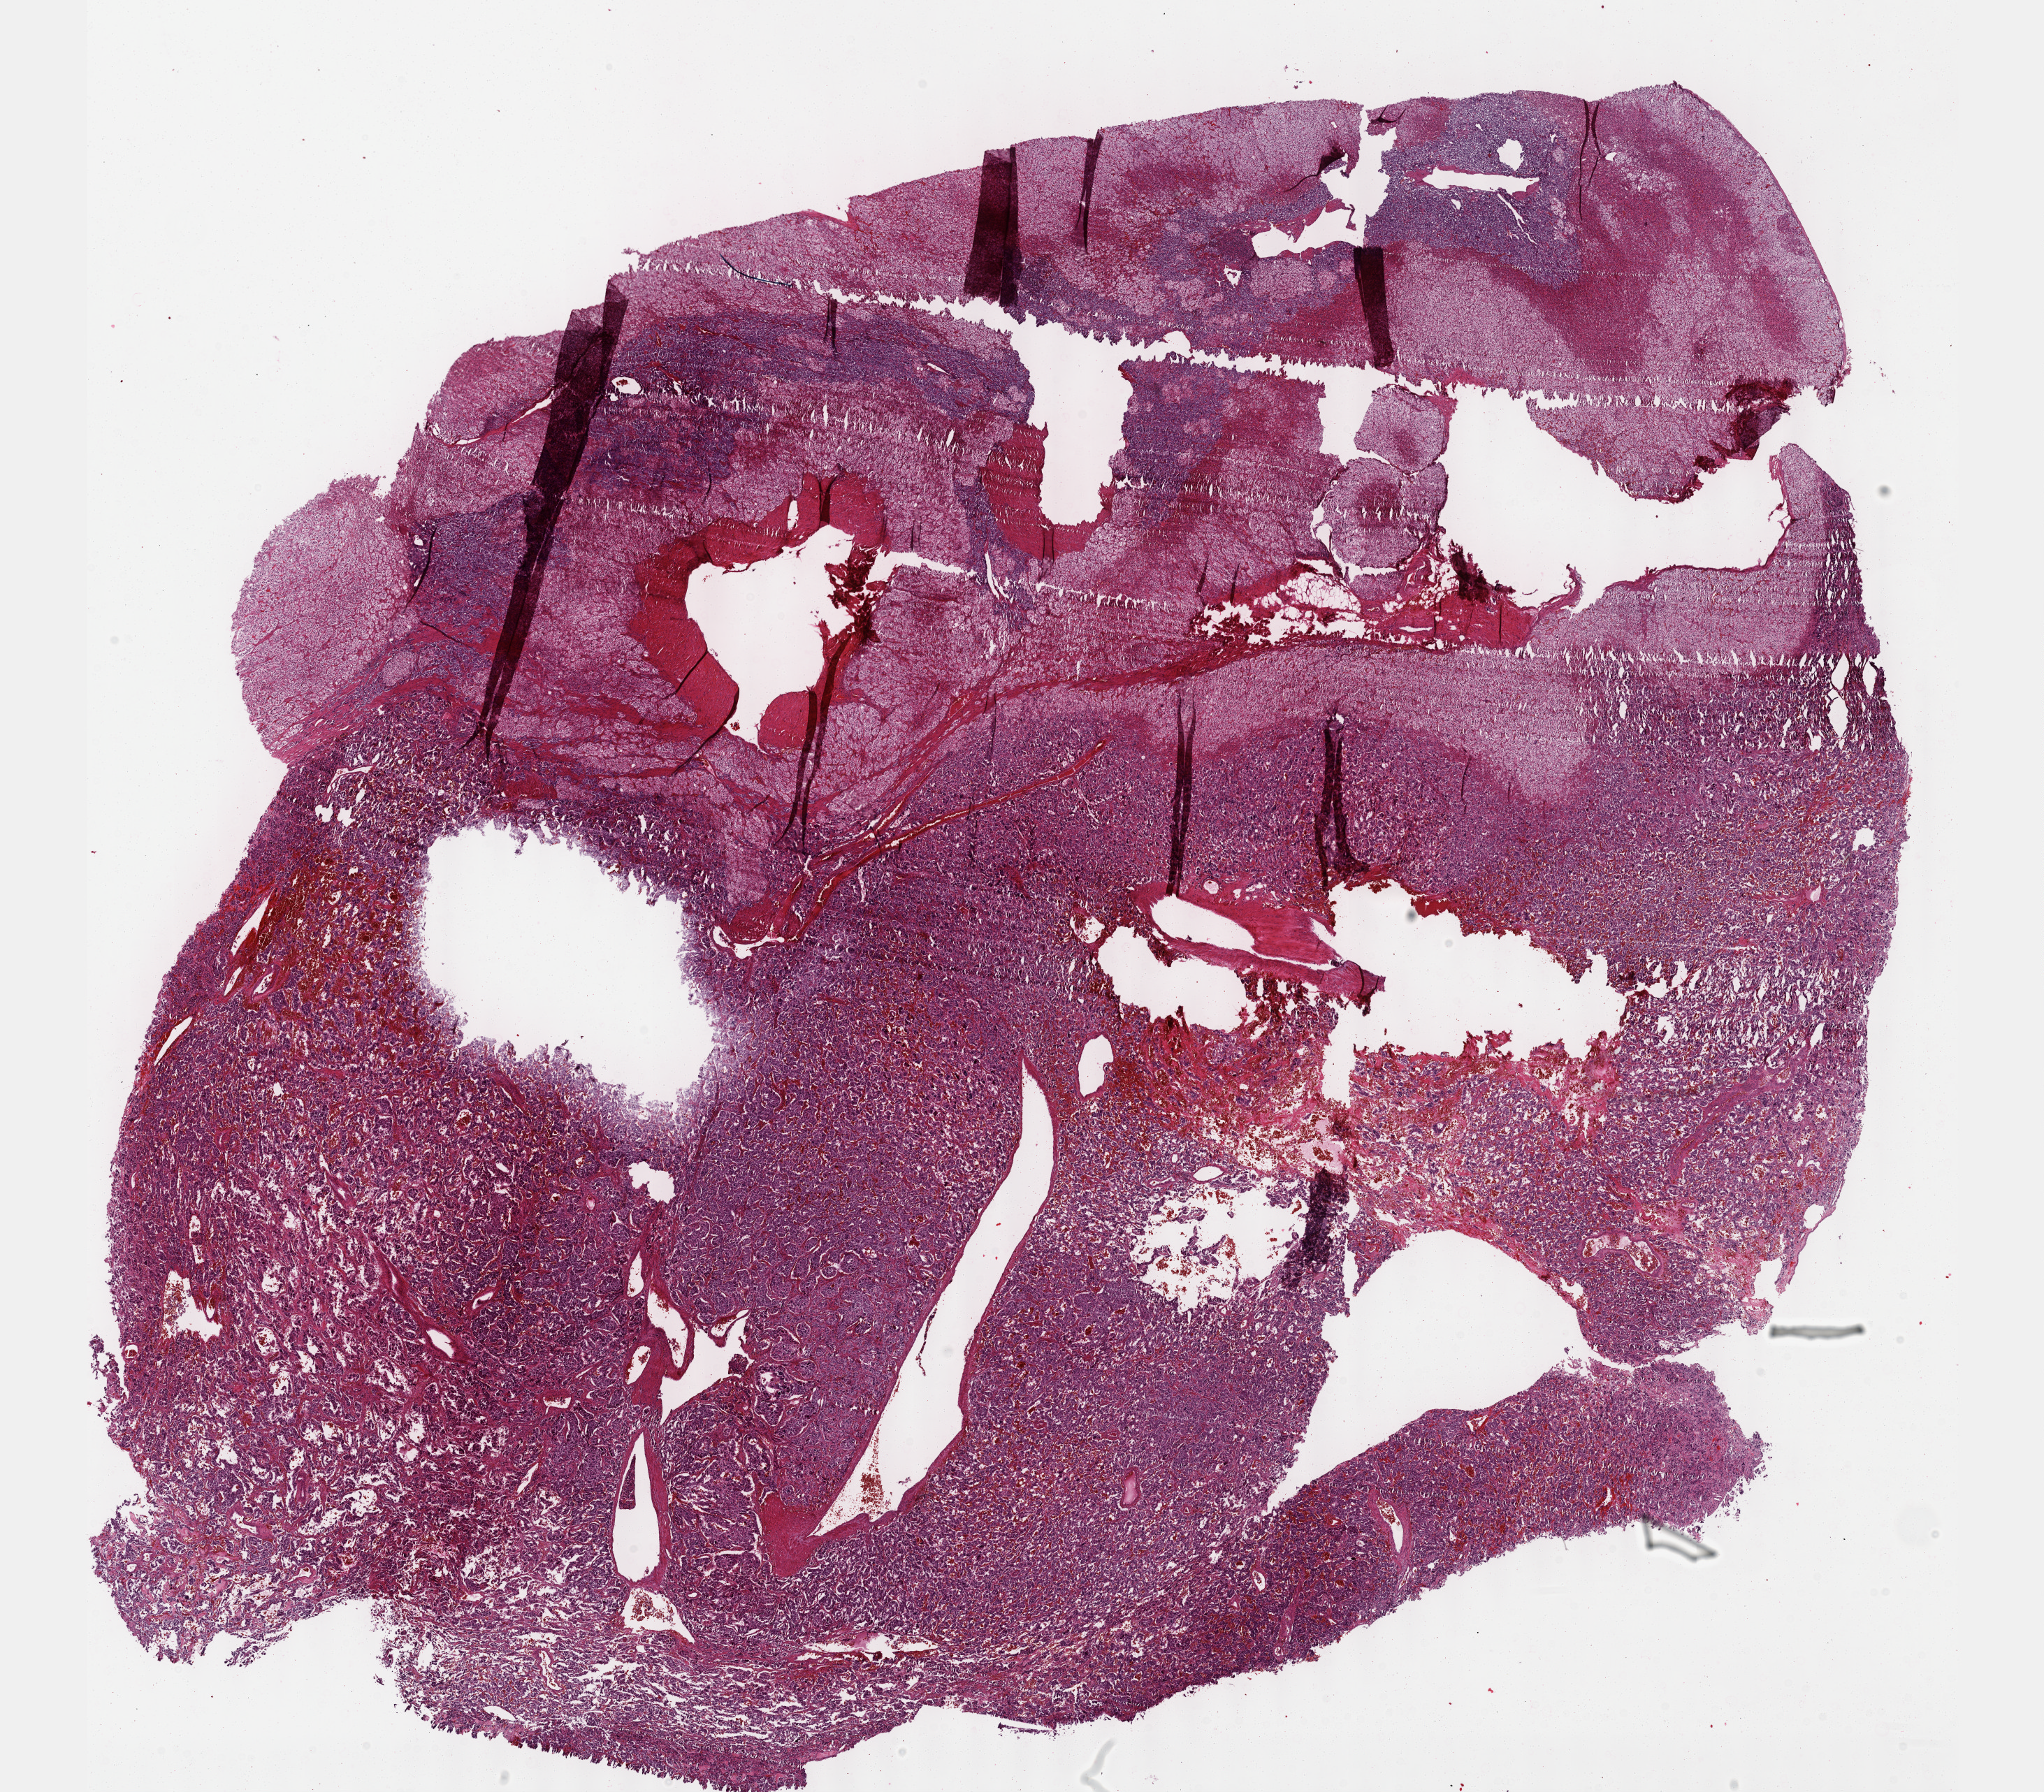
Digitized Hematoxylin and eosin (H&E) stained tissue section (whole slide), shown as a low-resolution overview of the whole scanned area (about 23.6 x 20.7 mm); FFPE section; sample: primary tumour, adrenal gland. Male, age 45 years at initial diagnosis.
* diagnosis: Pheochromocytoma, NOS
* laterality: left